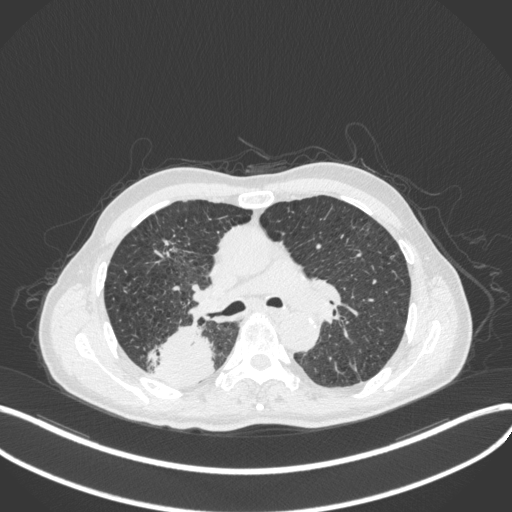
Chest CT, one axial slice. Position 285 of 423 along the scan axis. Reconstruction kernel B31f. 120 kVp. Lung window (W 1500 / L -600 HU). 1 mm slice thickness. 512 × 512 image matrix, field of view 400 × 400 mm. Patient: male, 79 years. Case-level facts recorded for this patient, not image findings: clinical TNM (as recorded): T3 N0 M0.
Structures marked on this image (rectangle marked by the reading radiologist):
- lung tumour (recorded histology: adenocarcinoma): bounding box <155,323,216,389> (left, top, right, bottom; pixels)